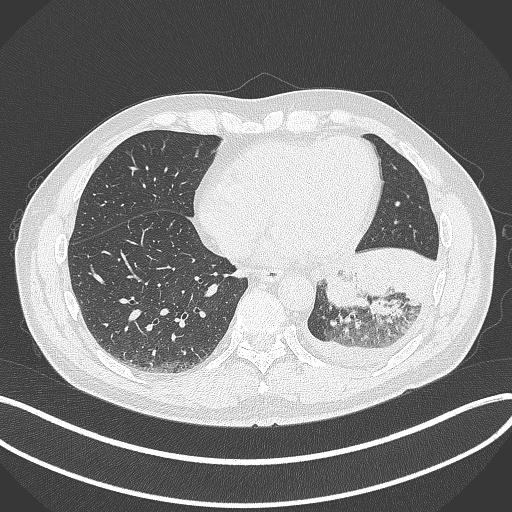
Chest CT, one axial slice; slice 114 of 342 in the series (ordered by position); reconstruction kernel B70f; lung window (W 1500 / L -600 HU); 1 mm slice thickness; 512 × 512 image matrix, field of view 400 × 400 mm. Patient: male, 58 years. Case-level facts recorded for this patient, not image findings: clinical TNM (as recorded): T3 N1 M1b.
Structures marked on this image (bounding box drawn by a radiologist):
- lung tumour (recorded histology: small cell carcinoma): bounding box (x1, y1, x2, y2) in pixels: (319, 264, 370, 311)